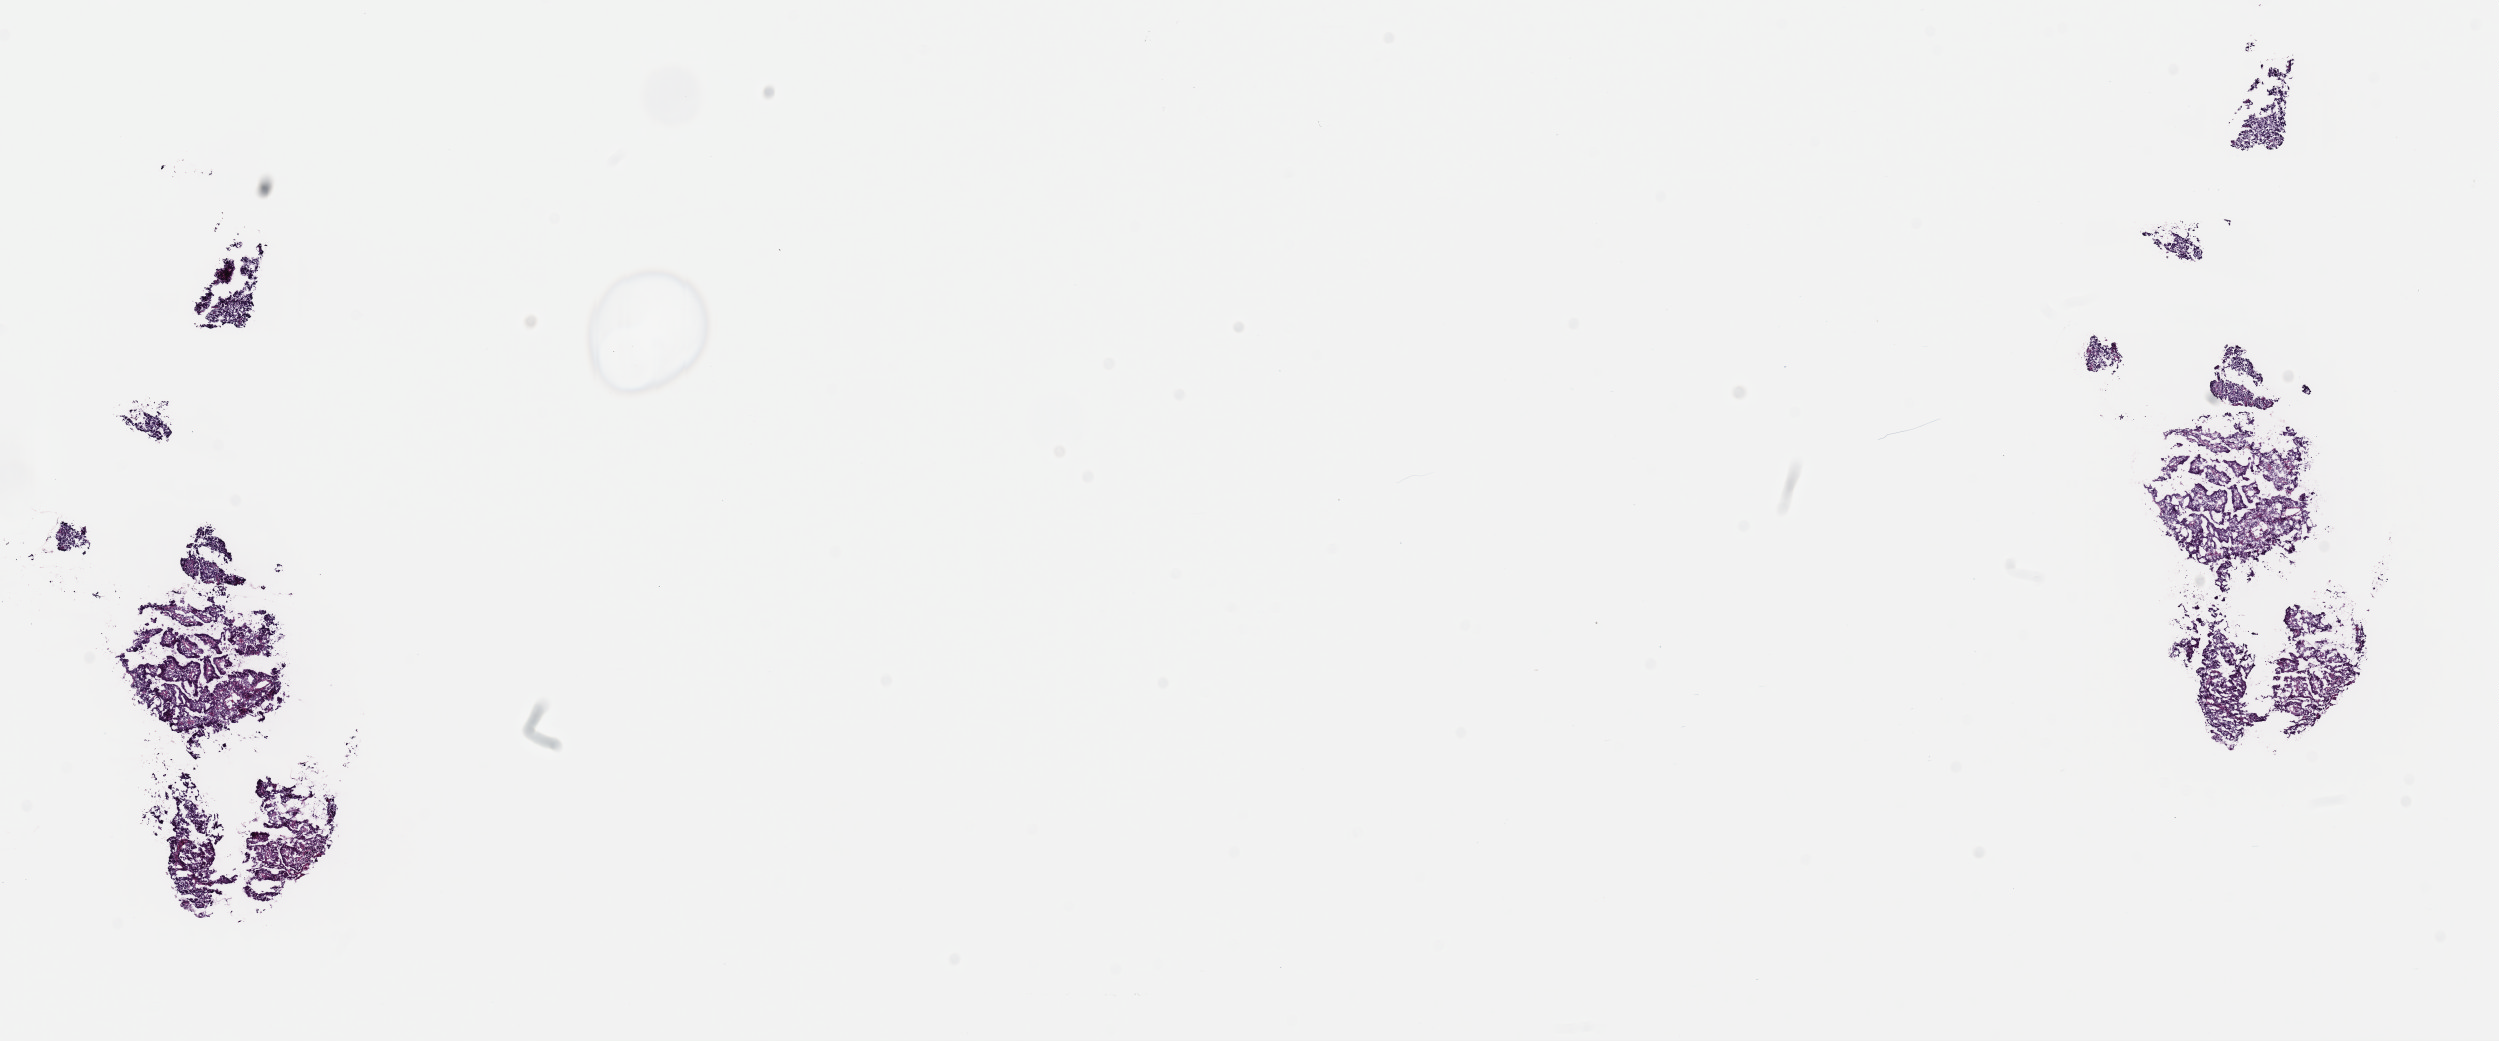
Hematoxylin and eosin (H&E) stained whole-slide image, shown as a low-resolution overview of the whole scanned area (about 19.7 x 8.2 mm), frozen section, cervix, primary tumour sample. Female patient; age at initial diagnosis 37 years. Histologic grade: G2 (moderately differentiated). Slide review estimates, as recorded: tumour cells 100%, tumour nuclei 70%, normal cells 0%, stromal cells 0%, necrosis 0%. Infiltration values recorded for this section: lymphocyte infiltration 0%, monocyte infiltration 0%, neutrophil infiltration 0%.
FIGO stage: IB1. Pathologic diagnosis: Adenocarcinoma, endocervical type (cervix uteri).